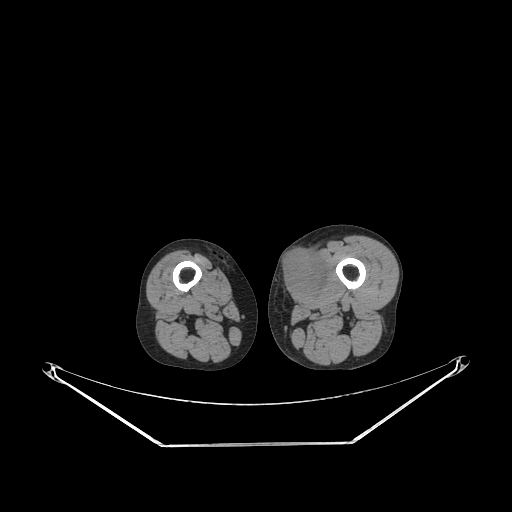
CT of an extremity soft-tissue mass (from a PET/CT study), one axial slice; position 214 of 267 along the scan axis; reconstruction kernel STANDARD; 140 kVp; soft-tissue window (W 400 / L 40 HU); 512 × 512 image matrix. Male patient. Case-level facts recorded for this patient, not image findings: histological type: pleiomorphic leiomyosarcoma; grade: high; site of the primary tumour: left thigh.
Annotated regions visible in this slice (expert contour drawn on MRI and transferred to this co-registered scan by the dataset authors):
- gross tumour volume including surrounding oedema: bounding box <281,251,328,298> (left, top, right, bottom; pixels)
- gross tumour volume (mass): <281,251,325,298>